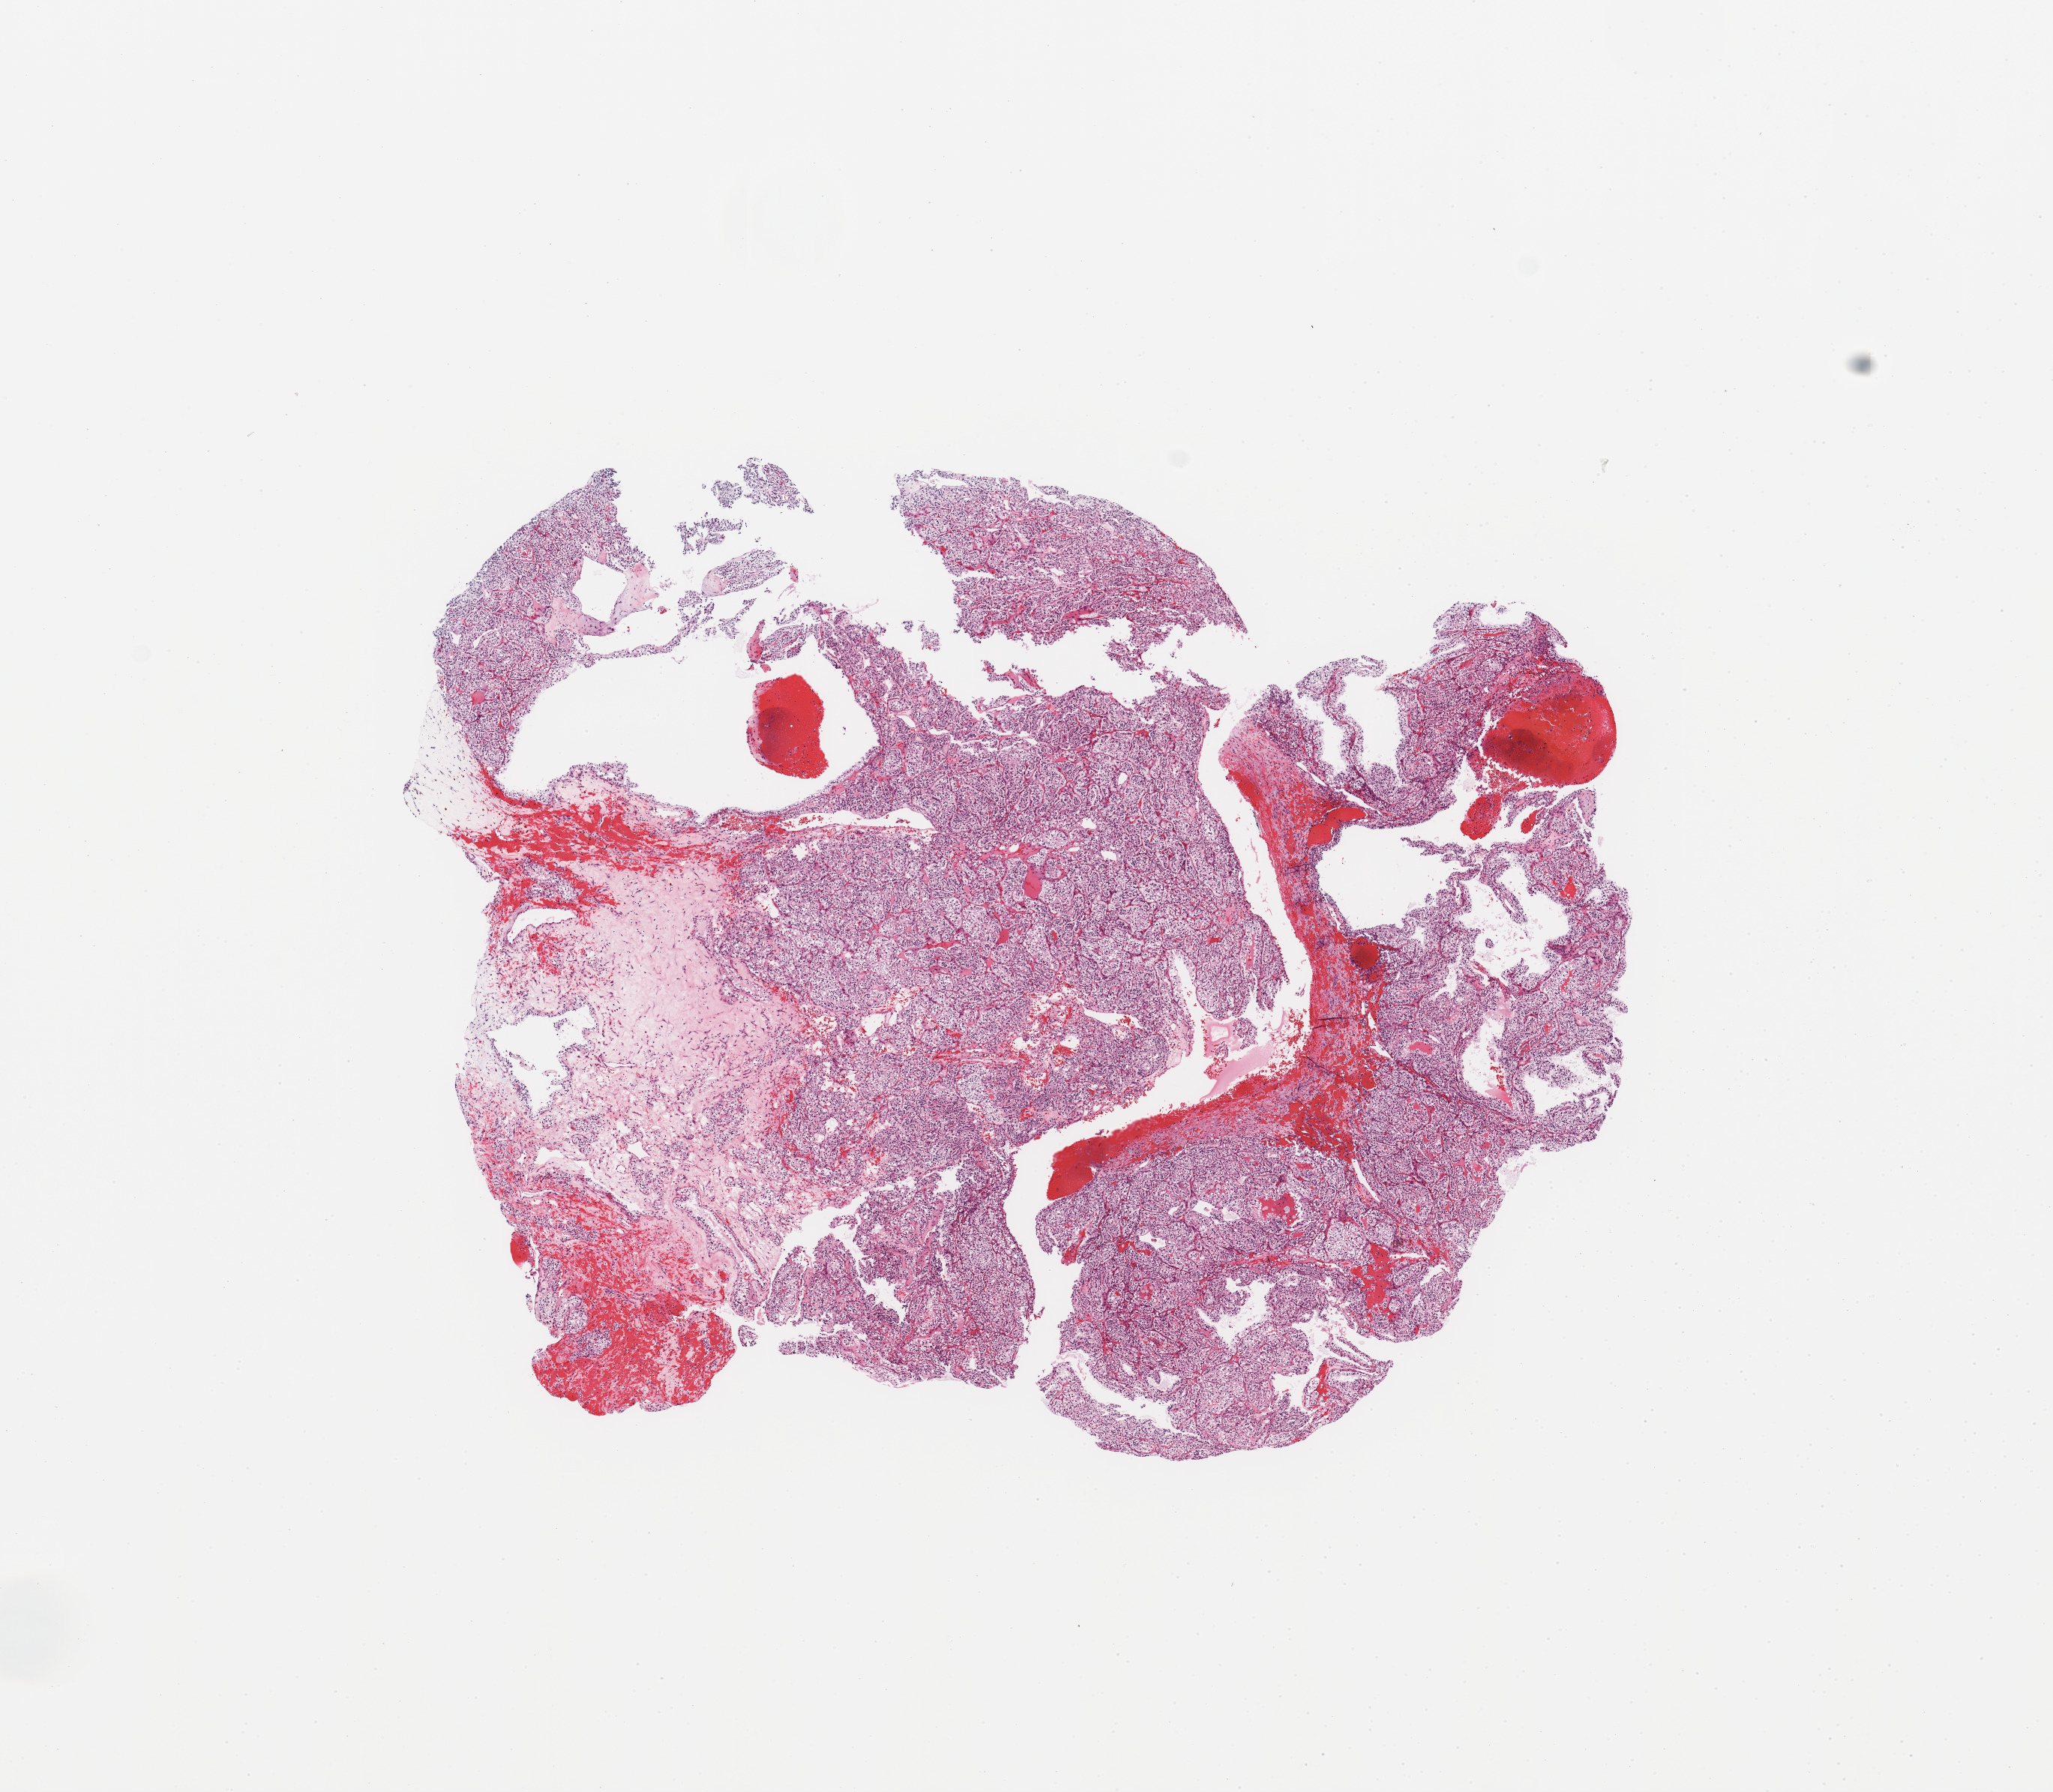
H&E-stained whole-slide image — a low-resolution overview of the entire scanned area, about 10.8 x 9.5 mm (acquisition: 20x scan); tumour tissue sample, sampled site: kidney. 35-year-old male patient. Histologic grade: G3 (poorly differentiated). Slide review estimates, as recorded: tumour nuclei 90%, necrosis 0%.
- AJCC pathologic stage: I
- diagnosis: Renal cell carcinoma, NOS
- primary tumour site (as recorded): upper pole